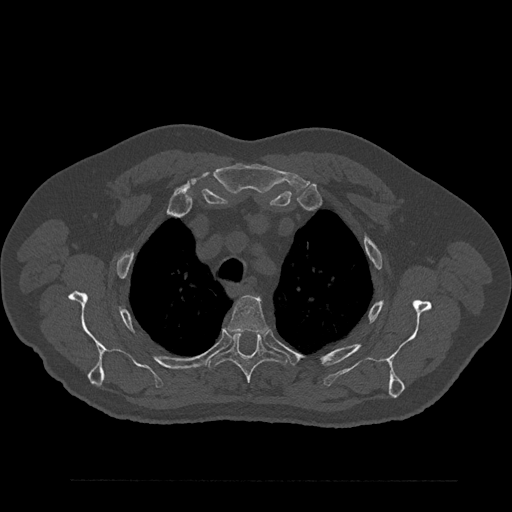
CT including the spine, one axial slice; slice 658 of 797 in the series (ordered by position); bone window (W 1800 / L 400 HU); 512 × 512 image matrix, field of view 430 × 430 mm. Patient: male, 61 years. Case-level facts recorded for this patient, not image findings: primary cancer: prostate.
Annotated regions visible in this slice (semi-automatic segmentation, software-assisted and operator-edited):
- T3 vertebra: box from (x=228, y=295) to (x=266, y=333) px
- T4 vertebra: (x=207, y=331)–(x=287, y=398)